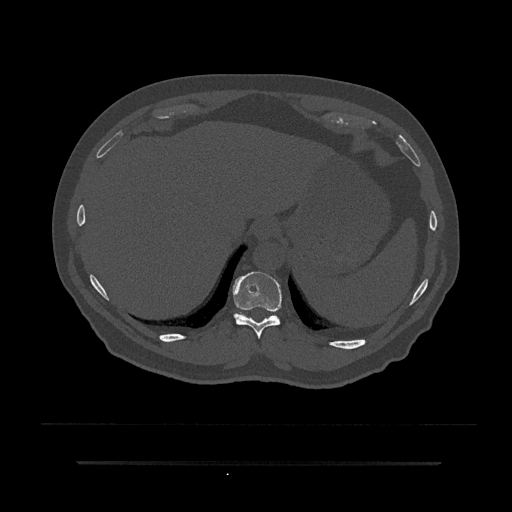
CT including the spine, one axial slice. Position 318 of 797 along the scan axis. 120 kVp. Bone window (W 1800 / L 400 HU). 0.5 mm slice thickness. 512 × 512 image matrix, field of view 464 × 464 mm. Male patient, age 59 years. Case-level facts recorded for this patient, not image findings: primary cancer: bile ducts; vertebrae with lytic lesions (as recorded): T10.
Annotated regions visible in this slice (semi-automatic segmentation, software-assisted and operator-edited):
- T10 vertebra: bounding box <233,271,282,338> (left, top, right, bottom; pixels)
- T11 vertebra: <236,313,274,320>